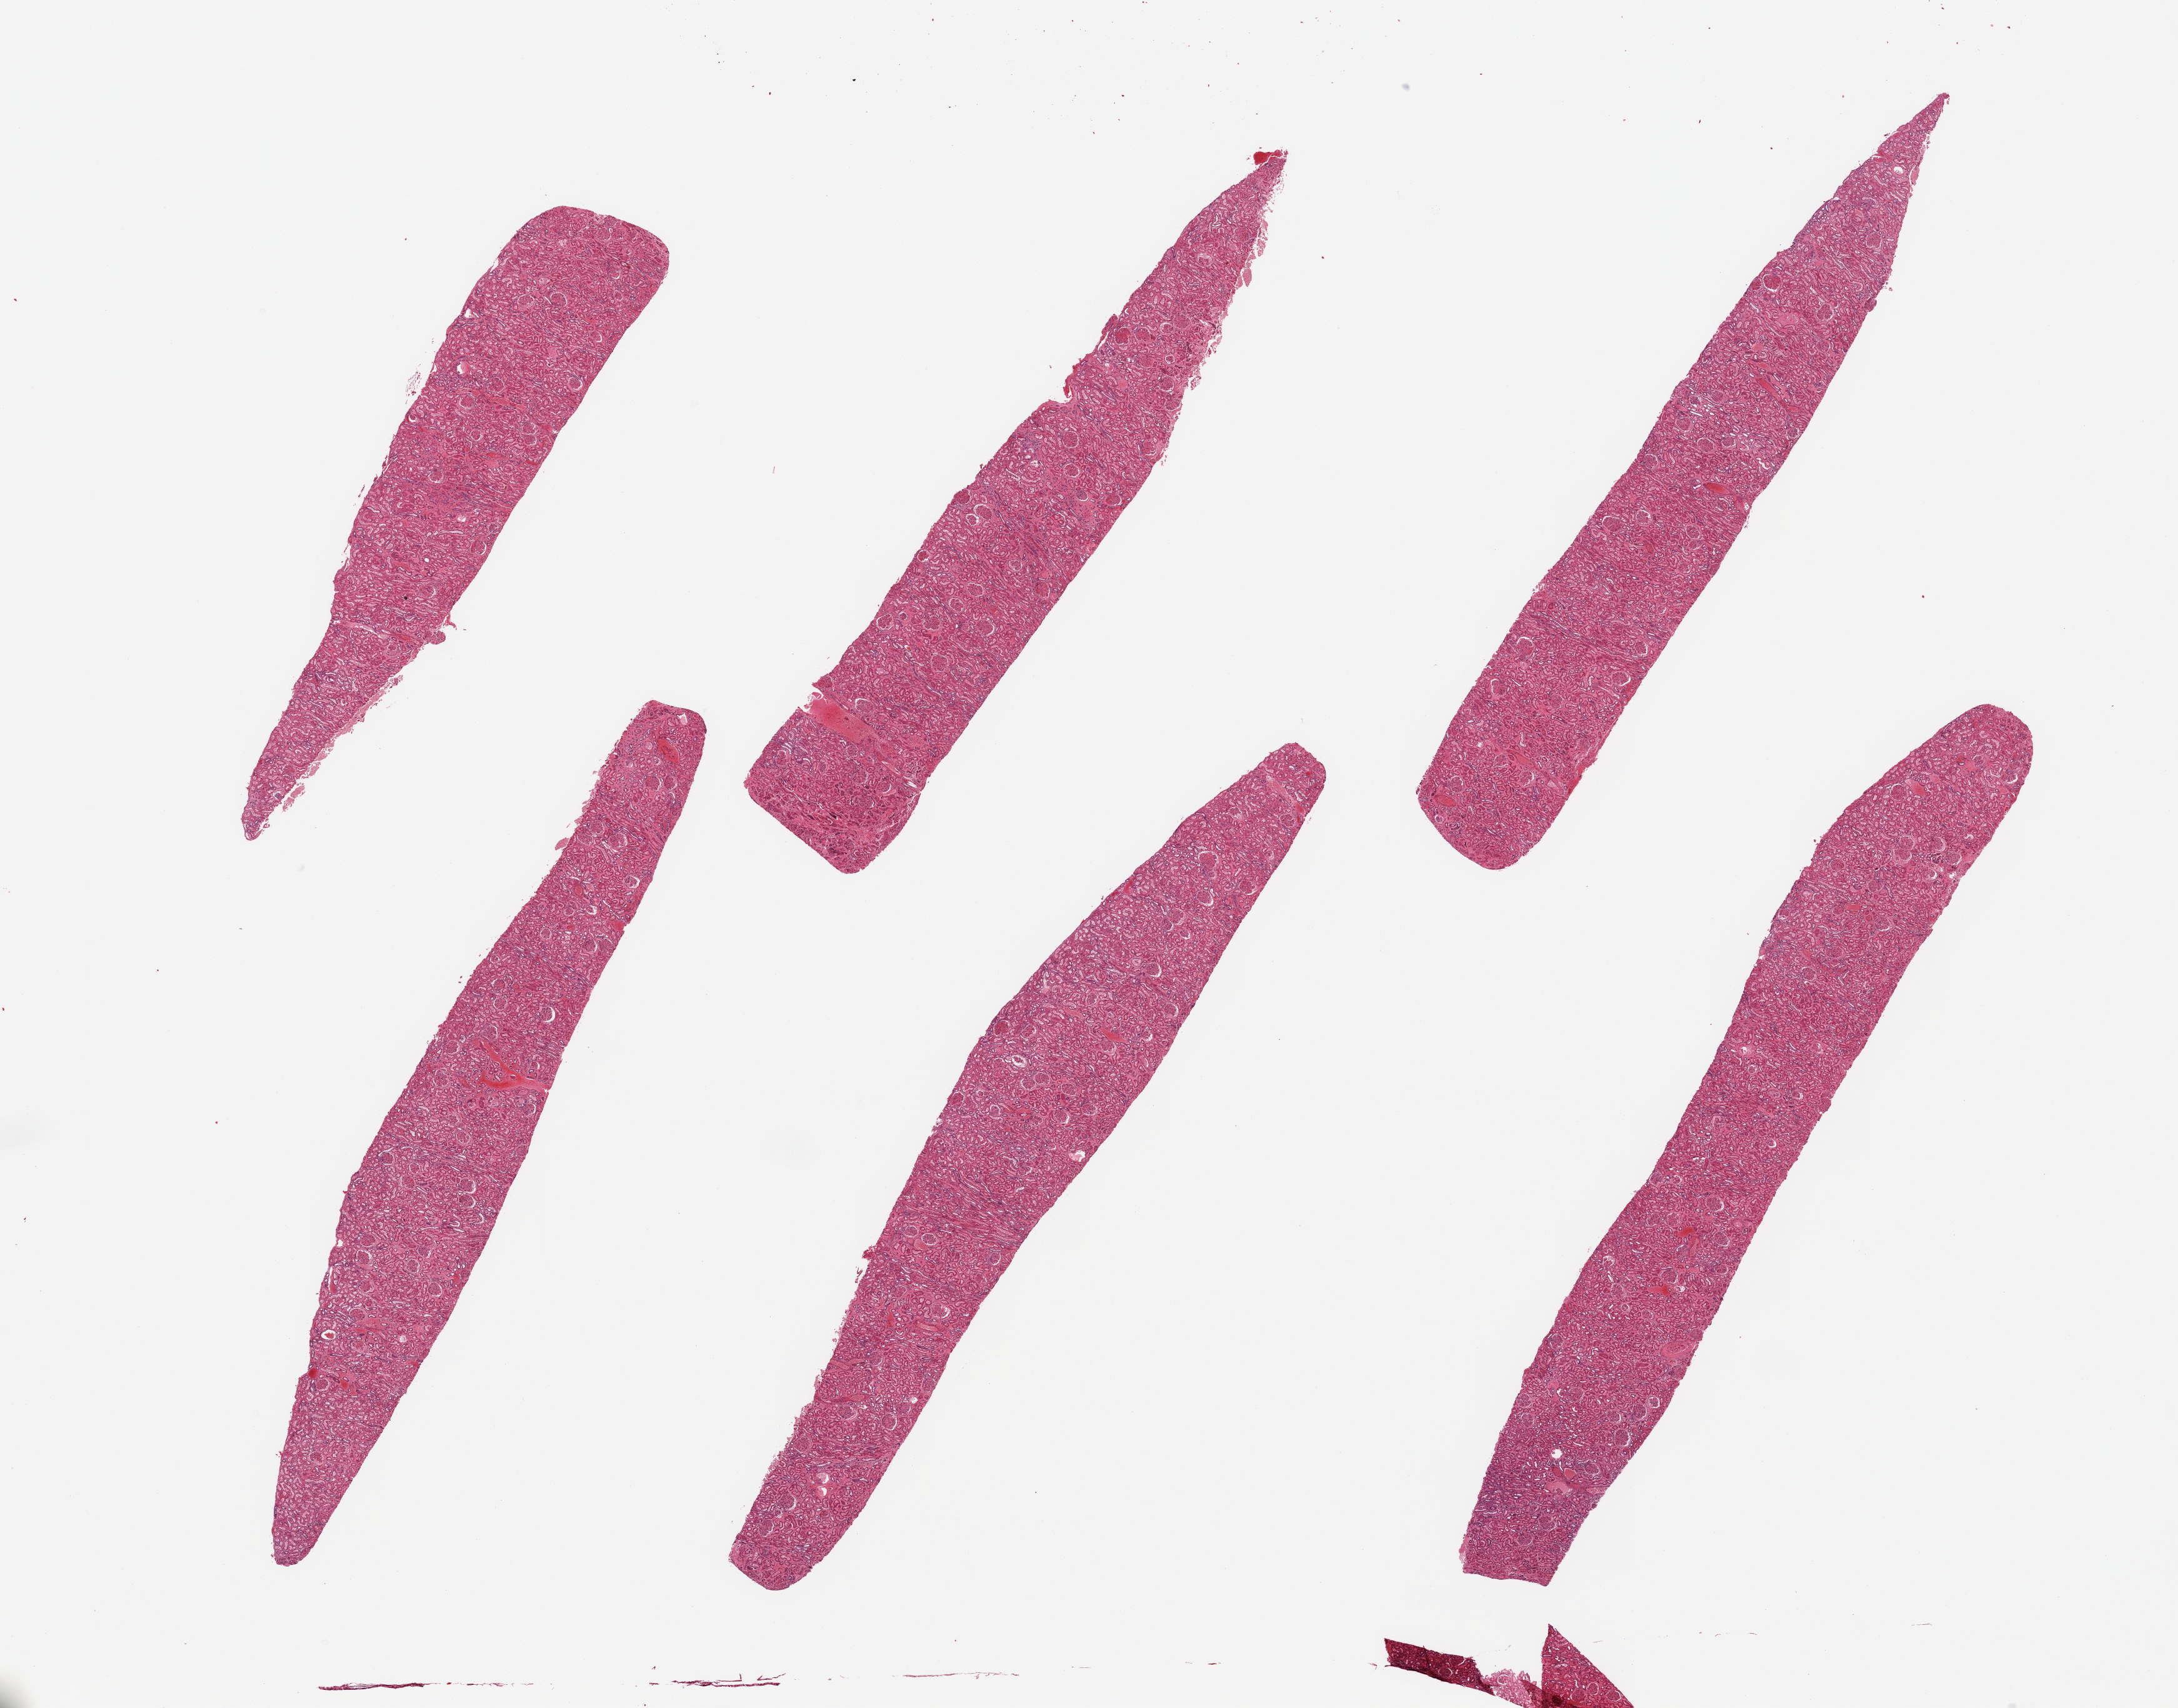
Digitized haematoxylin and eosin-stained section, whole scanned area (about 27.6 x 21.6 mm) shown as a low-resolution overview, PAXgene-fixed, paraffin-embedded tissue, sampled site (target tissue): renal cortex, donor tissue sample. Male donor.
Review note (as recorded): 6 pieces; congestion, glomeruli in all sections.